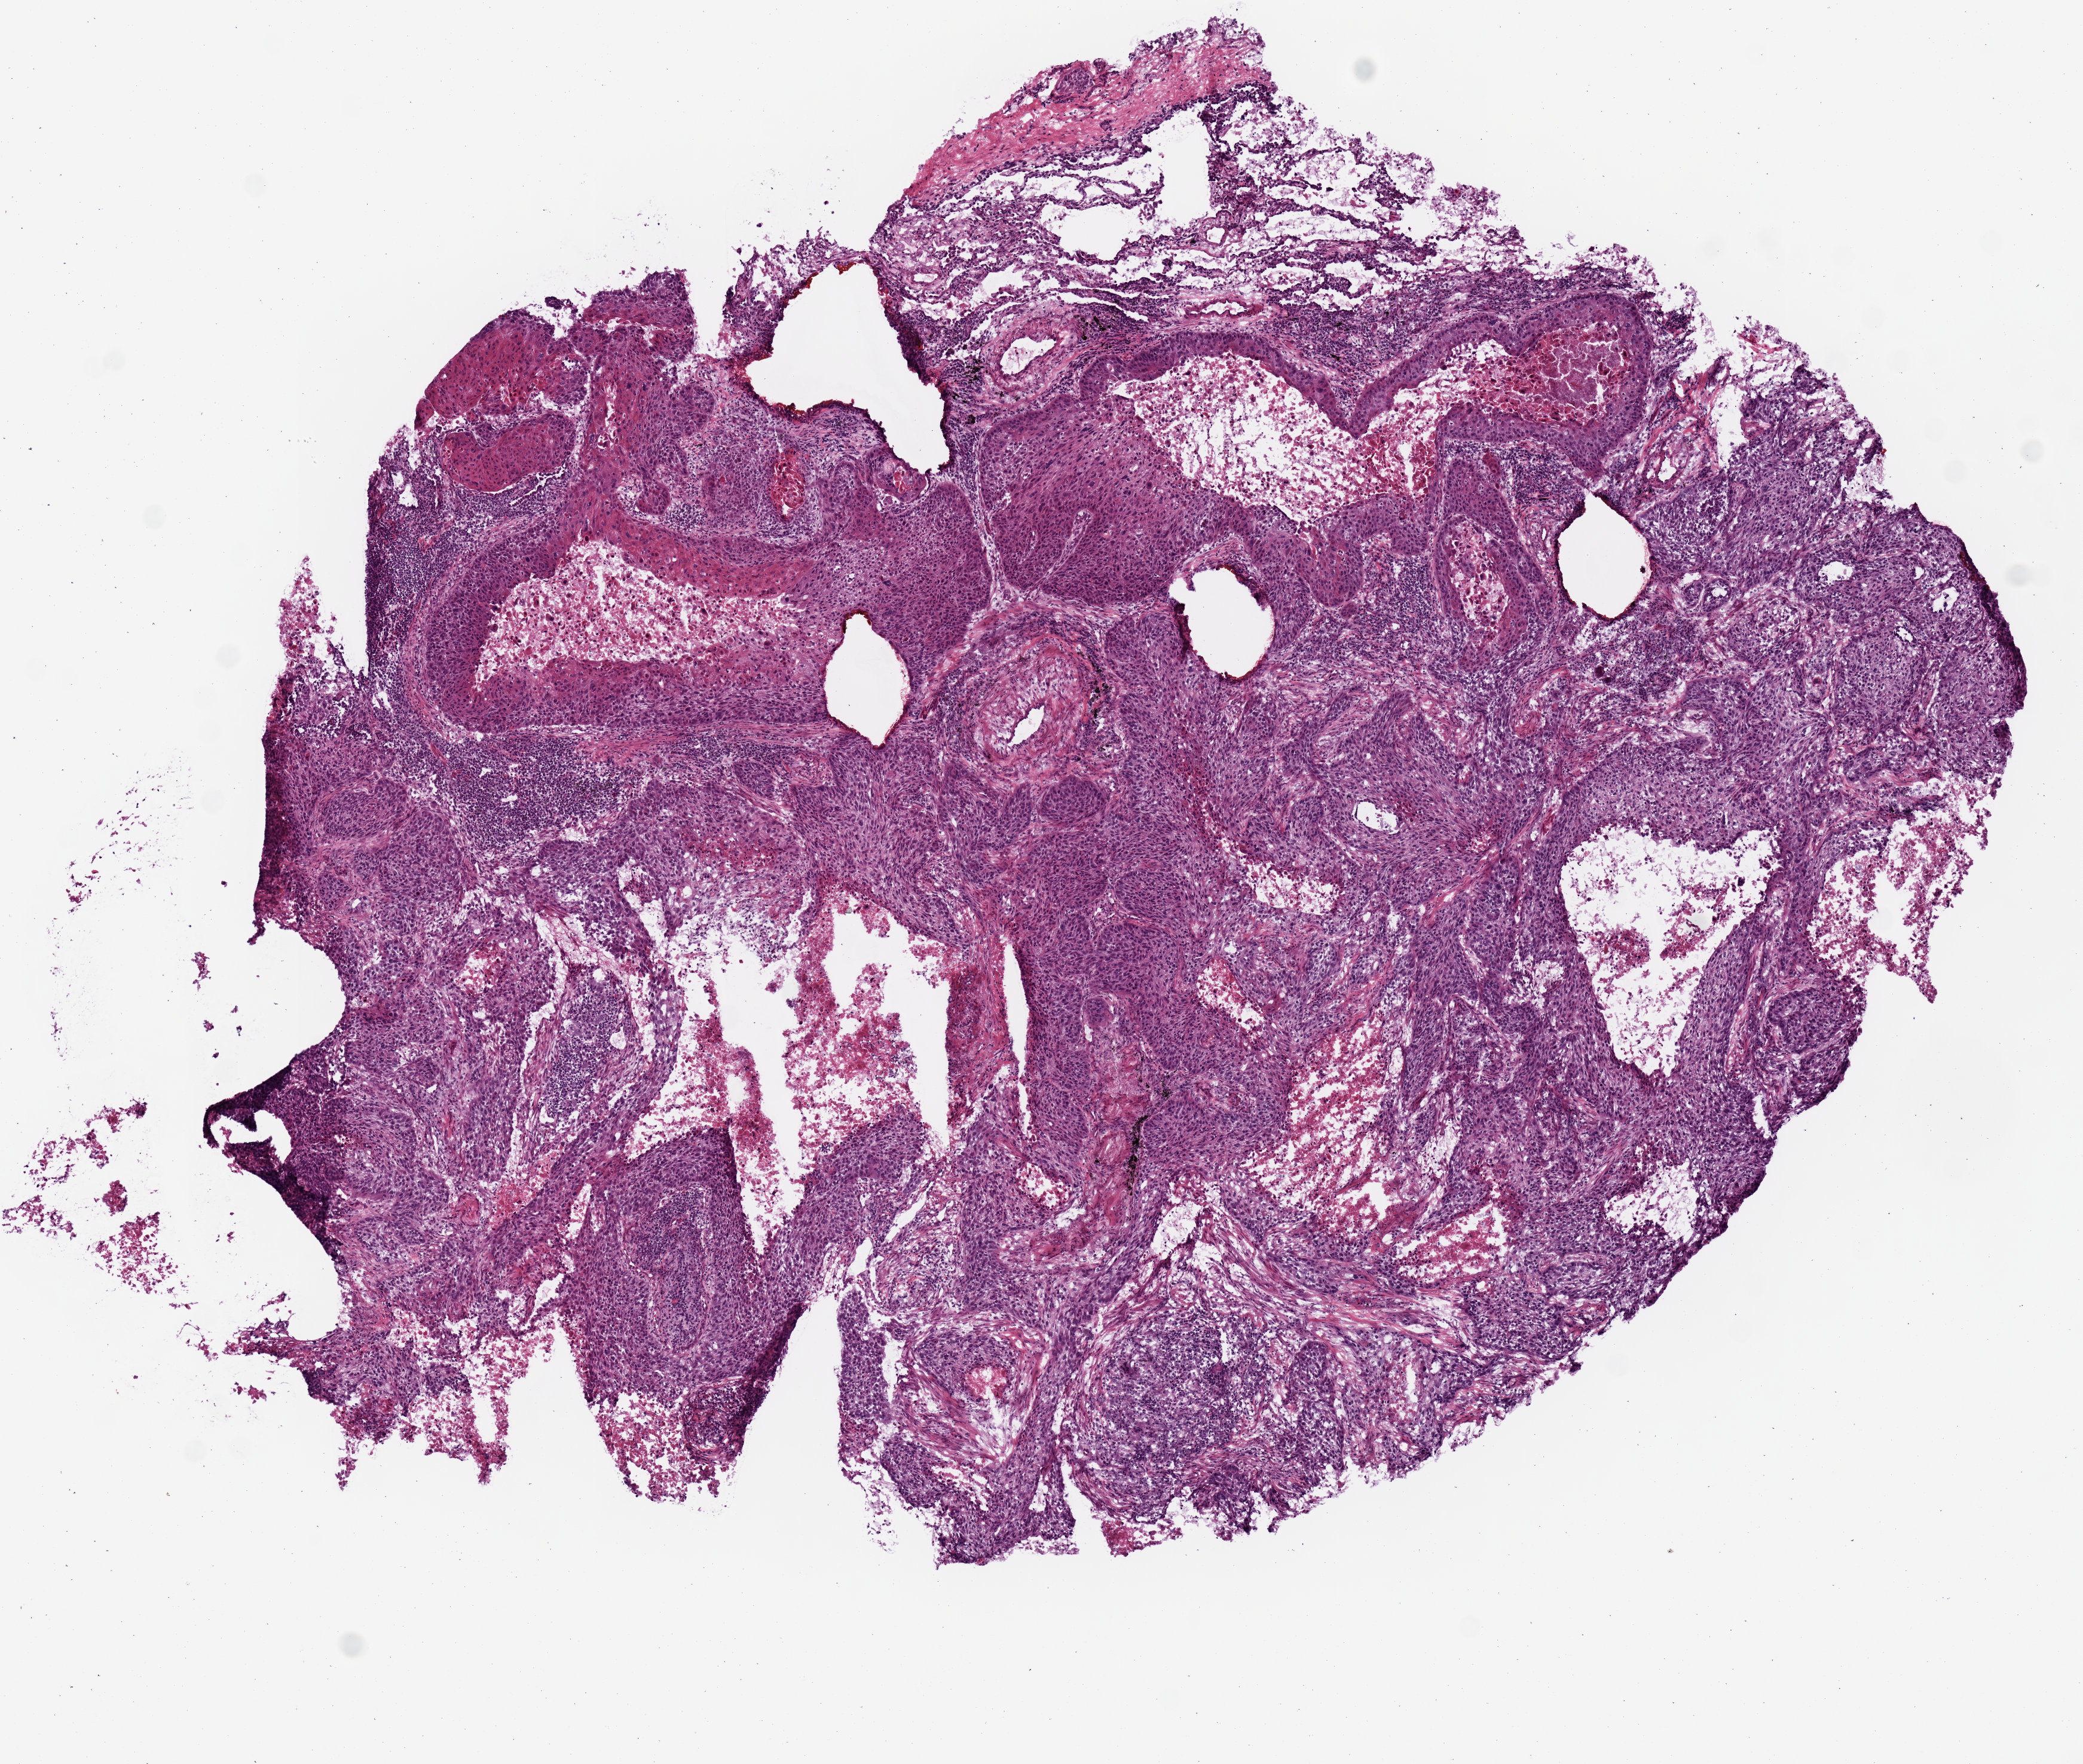
Hematoxylin and eosin (H&E) stained whole-slide image — shown as a low-resolution overview of the whole scanned area (about 6.9 x 5.8 mm, from a 20x scan). Frozen section. Sample: primary tumour, lung. Male patient; age at initial diagnosis 79 years. Slide review estimates, as recorded: tumour cells 85%, tumour nuclei 75%, normal cells 0%, stromal cells 10%, necrosis 5%.
Laterality: left. Histologic diagnosis: Squamous cell carcinoma, NOS (upper lobe, lung). AJCC pathologic stage: IIB (7th edition).